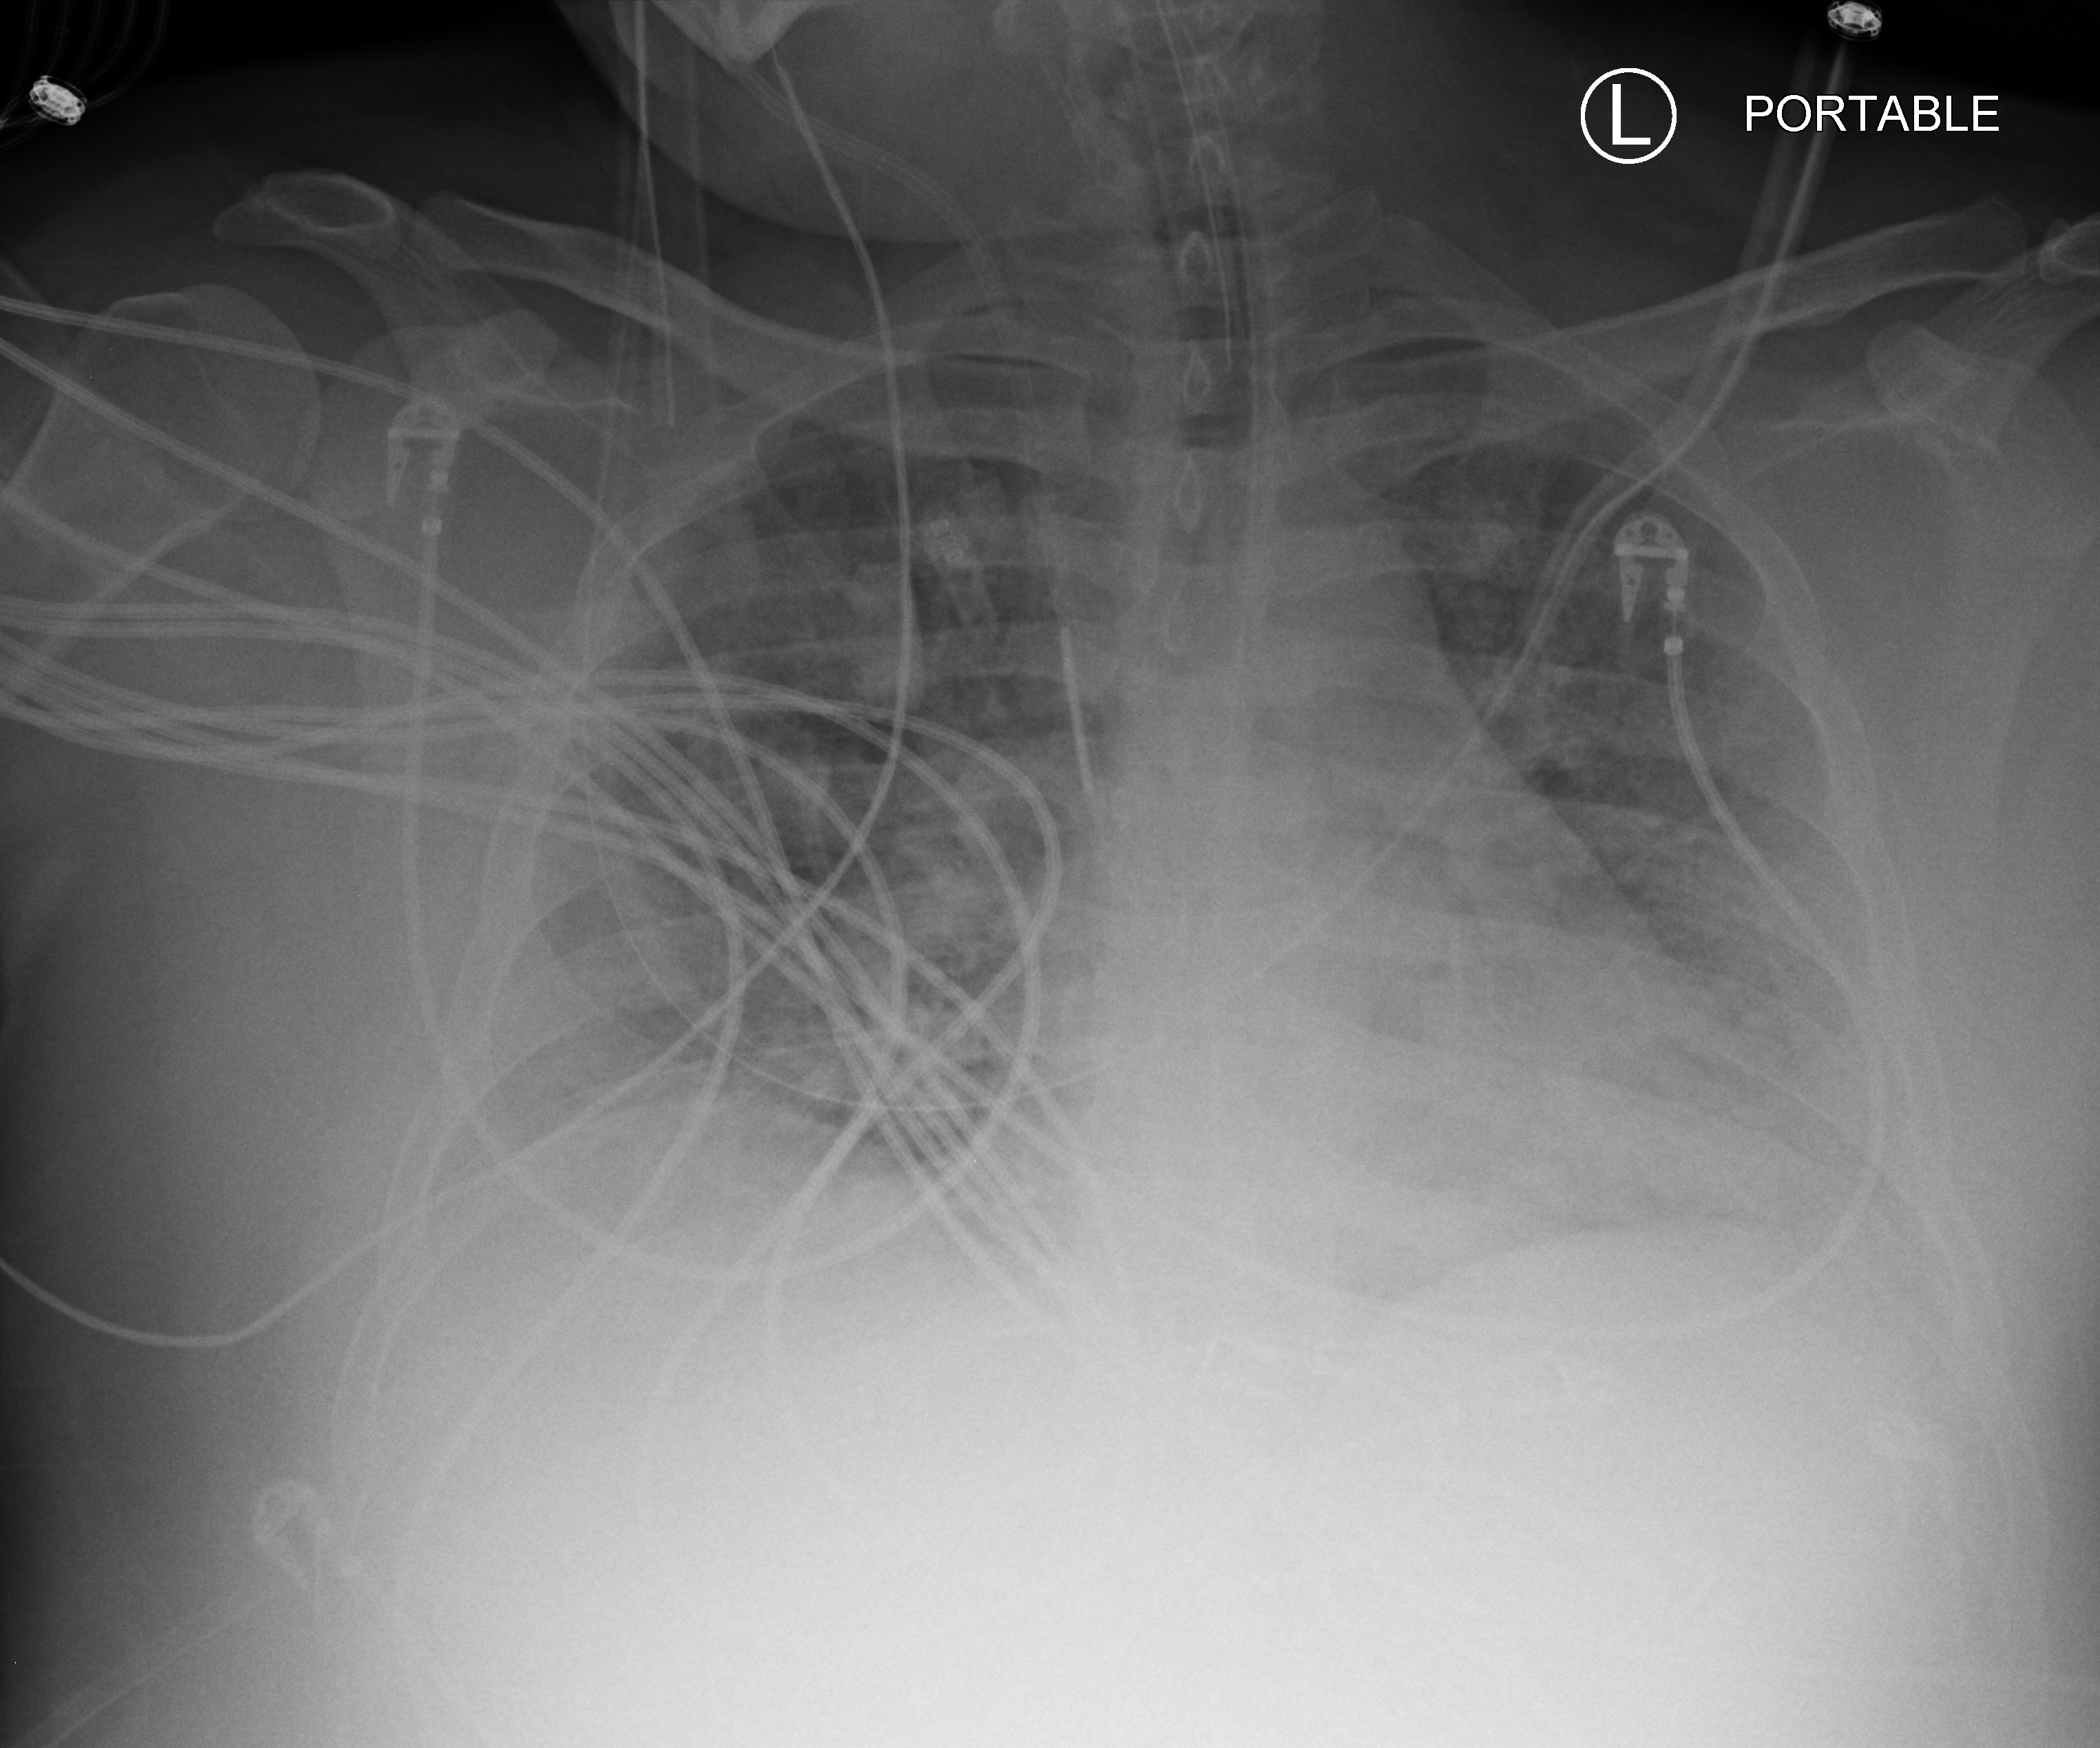
Bedside chest radiograph (computed radiography), anteroposterior (AP) projection. Patient hospitalised with COVID-19, aged 18–59 years.
Hospital-stay facts (about this admission, not read from this image; timing relative to this image not recorded): mechanically ventilated during this hospital stay: yes; length of hospital stay: 22 days.